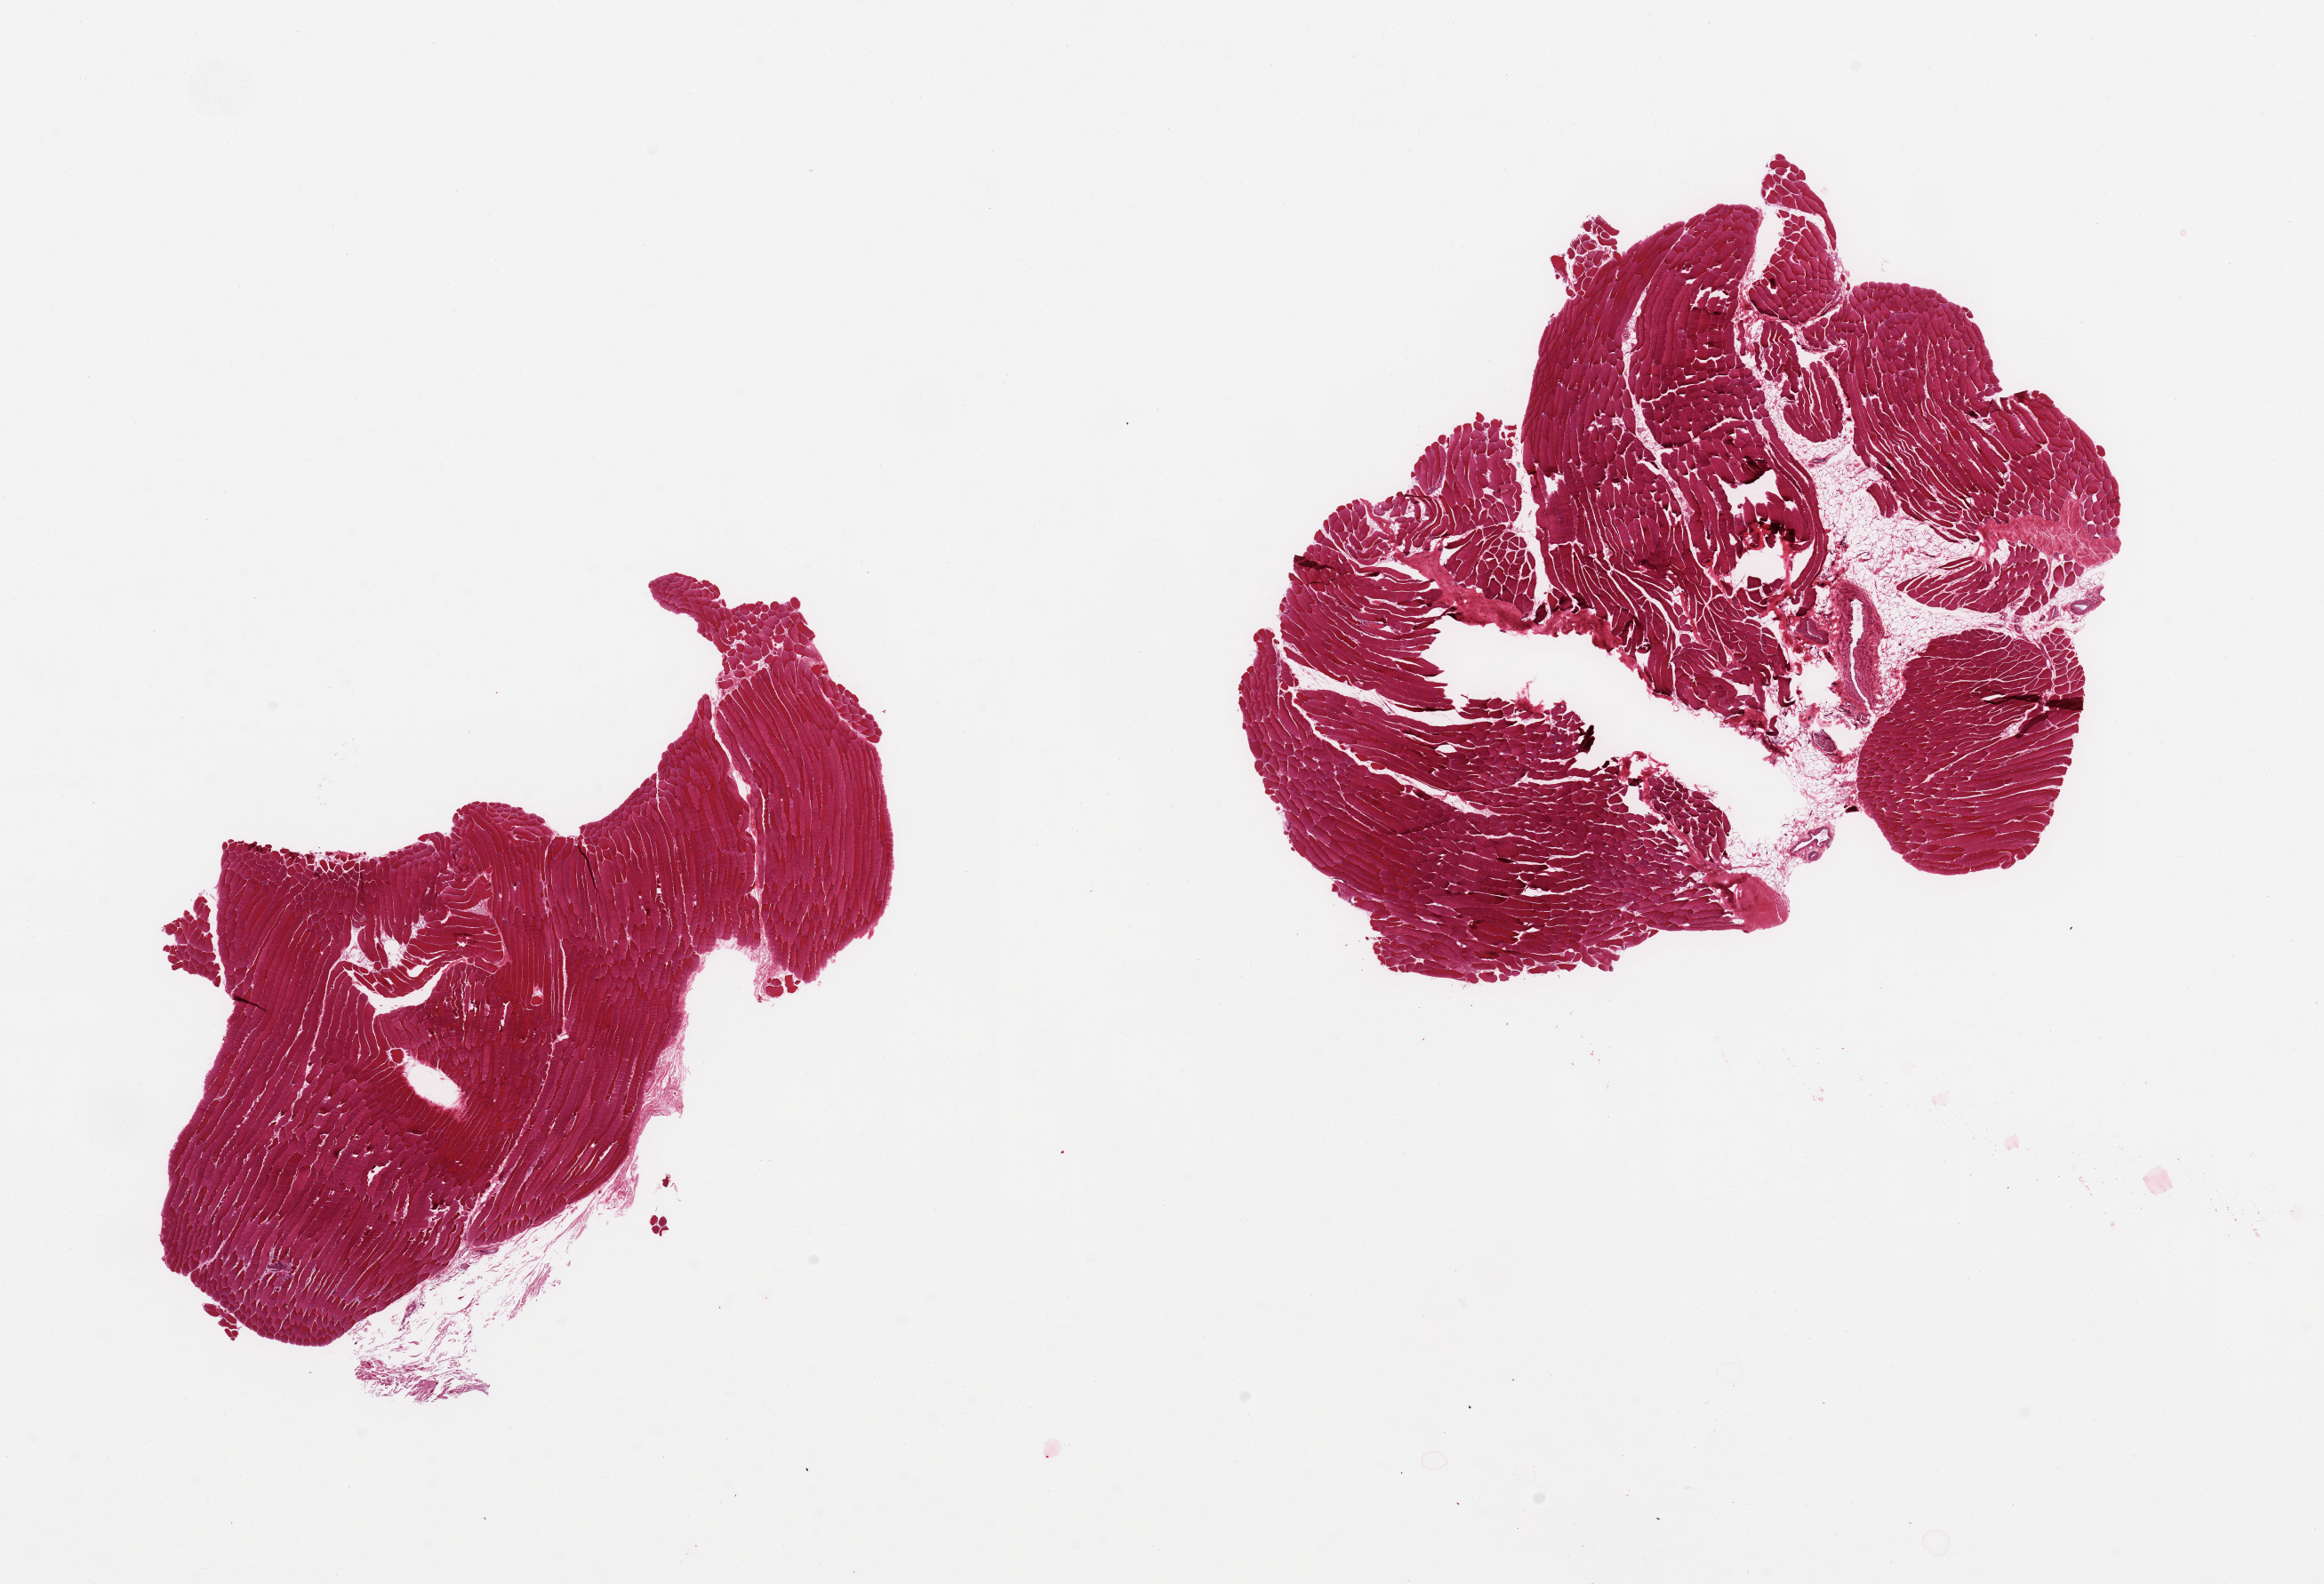
H&E whole-slide image, brightfield — a low-resolution overview of the entire scanned area, about 20.7 x 14.1 mm (acquisition: 20x scan). PAXgene-fixed paraffin-embedded (PFPE) section. Sampled site (target tissue): skeletal muscle. Tissue donor sample. Donor: male.
• reviewer comment on this tissue sample: 2 pieces, interstitial fat/vascular elements are ~10% of tissue